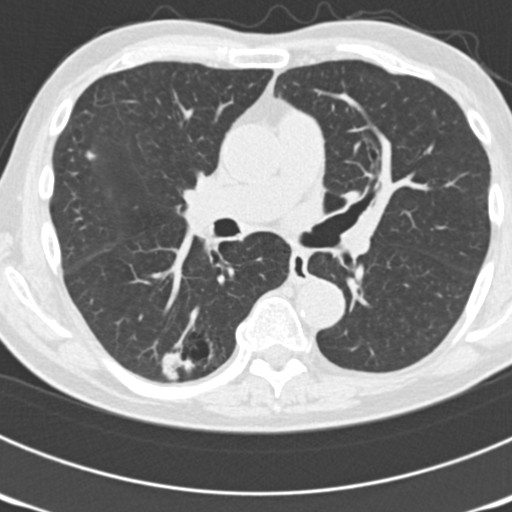
Low-dose screening chest CT, one axial slice; position 105 of 177 along the scan axis; reconstruction kernel B30f; lung window (W 1500 / L -600 HU); 512 × 512 image matrix.
Annotated regions visible in this slice (outlined manually by an expert reader):
- lesion 2 (nodule, upper lobe of right lung): box from (x=86, y=151) to (x=96, y=160) px
- lesion 5 (nodule, lower lobe of right lung): (x=163, y=352)–(x=194, y=377)